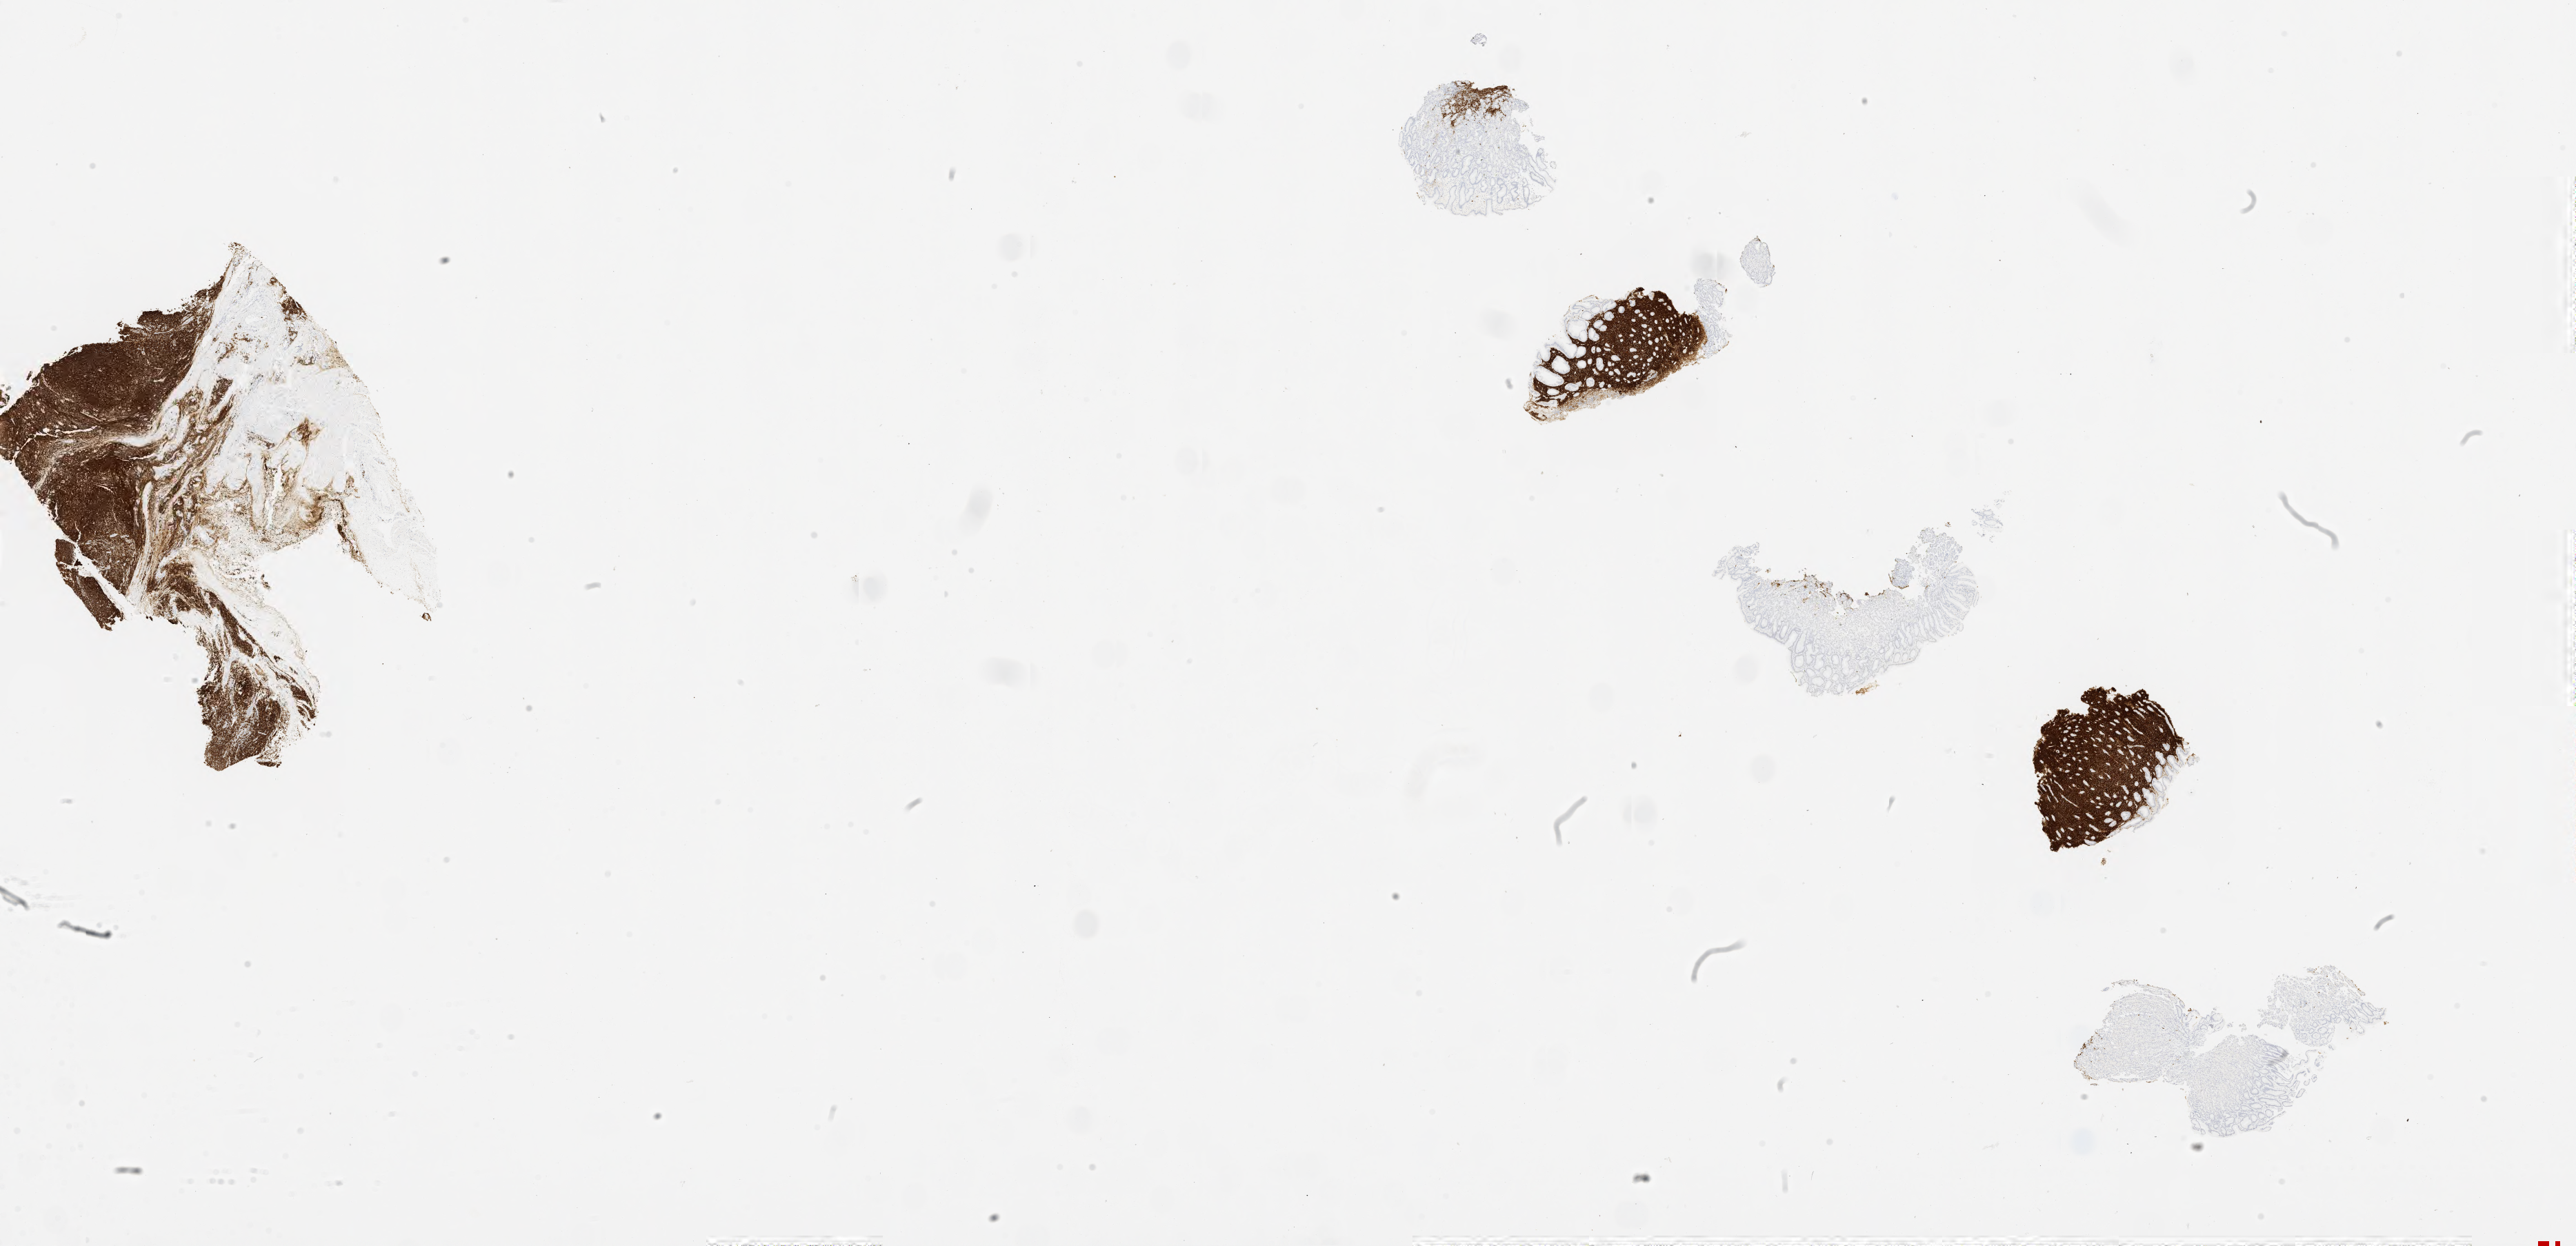
Immunohistochemistry (IHC) whole-slide image stained for CD20 — shown as a low-resolution overview of the whole scanned area (about 30.0 x 14.5 mm), specimen: tumor tissue. Male patient, aged 40.
Histologic diagnosis: Burkitt lymphoma, NOS.